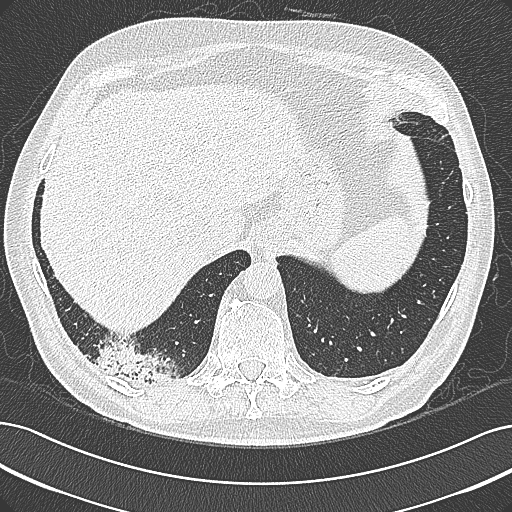
Chest CT (low-dose screening protocol), one axial image. Baseline screening round. Lung window (W 1500 / L -600 HU). 1 mm slice thickness. Male participant, aged 68 years at enrolment.
Expert-annotated lung lesion, bounding box (x1, y1, x2, y2) in pixels: (95, 338, 192, 399). Screening reader's record for this exam: no non-calcified nodule ≥4 mm recorded. Official screen result: negative screen, significant abnormalities not suspicious for lung cancer.